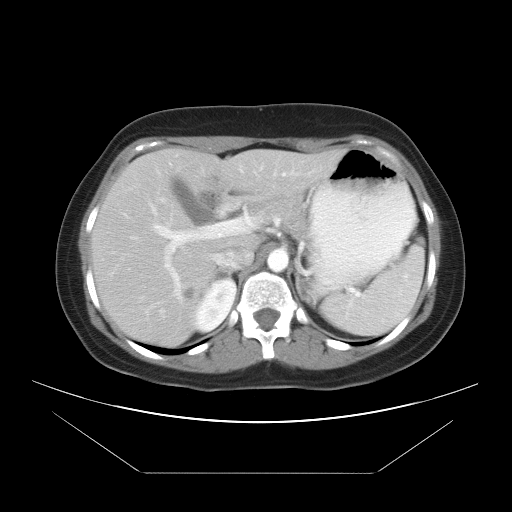
Contrast-enhanced abdominal CT, one axial slice; position 25 of 34 along the scan axis; soft-tissue window (W 400 / L 40 HU); 512 × 512 image matrix. Female patient, age 38 years. From the clinical record (not read from this slice): diagnosis: colorectal cancer liver metastases, imaged before liver resection; multiple liver metastases: yes; largest metastasis: 3.1 cm; disease in both lobes: no.
Outlined on this slice (manually delineated by an expert):
- liver: bounding box <90,149,345,347> (left, top, right, bottom; pixels)
- planned liver remnant (the part of the liver to remain after resection): <201,150,345,253>
- portal vein (with intrahepatic branches): <150,173,285,297>
- liver metastasis: <184,287,197,299>